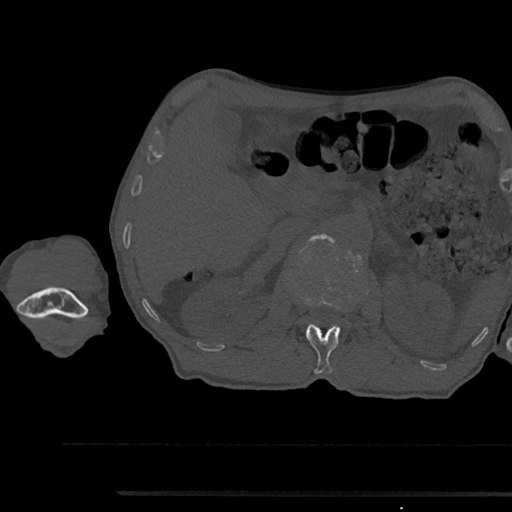
CT including the spine, one axial slice; reconstruction kernel Br40s/3; bone window (W 1800 / L 400 HU); 0.5 mm slice thickness; 512 × 512 image matrix, field of view 367 × 367 mm. Patient: male, 79 years. From the clinical record (not read from this slice): primary cancer: prostate.
Structures marked on this image (semi-automatic segmentation, software-assisted and operator-edited):
- L1 vertebra: bounding box [x1, y1, x2, y2] px = [295, 296, 340, 374]
- L2 vertebra: [308, 234, 335, 305]